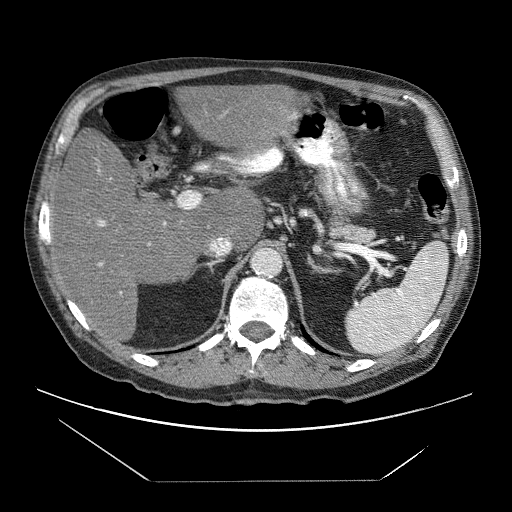
Contrast-enhanced abdominal CT (liver protocol), one axial slice; slice 37 of 83 in the series (ordered by position); reconstruction kernel STANDARD; soft-tissue window (W 400 / L 40 HU); 2.5 mm slice thickness; 512 × 512 image matrix, field of view 420 × 420 mm. From the clinical record (not read from this slice): diagnosis: hepatocellular carcinoma (patient treated with transarterial chemoembolisation; whether this scan precedes or follows treatment is not stated here); TNM stage (as recorded): Stage-IVB; Child-Pugh class: B; tumour nodularity: uninodular.
Annotated regions visible in this slice (semi-automatically segmented with operator editing):
- liver parenchyma outside the tumour (the mass and vessels are separate outlines, so this box may not span the whole liver): bounding box [x1, y1, x2, y2] px = [50, 84, 298, 342]
- liver vessels: [98, 113, 297, 294]